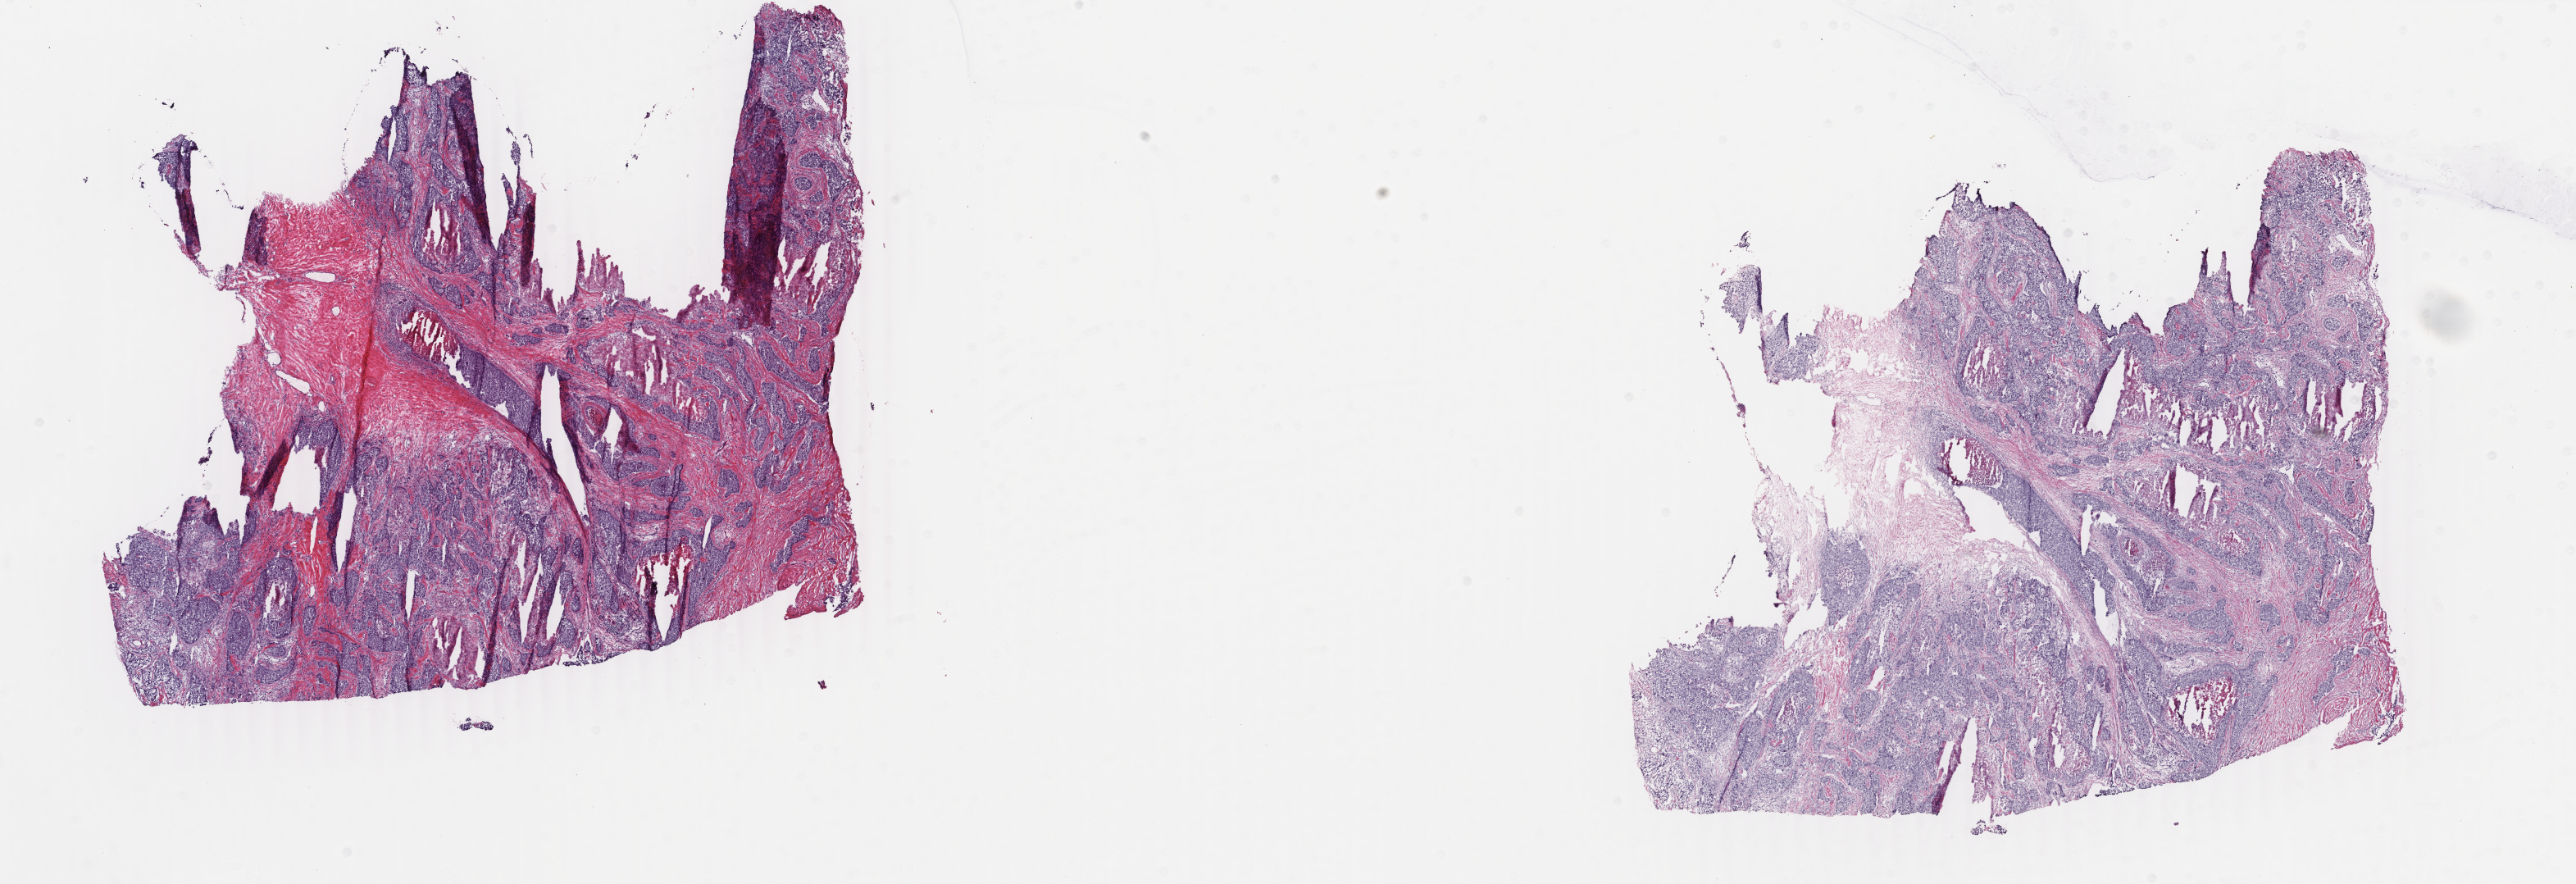
Digitized H&E tissue section (whole slide) — whole scanned area (about 25.0 x 8.6 mm, acquisition: 40x scan) shown as a low-resolution overview. Frozen section. Sample: primary tumour, breast. Female patient; age at initial diagnosis 51 years. Slide review estimates, as recorded: tumour cells 50%, tumour nuclei 80%, normal cells 0%, stromal cells 15%, necrosis 35%. Infiltration values recorded for this section: lymphocyte infiltration 3%, monocyte infiltration 0%, neutrophil infiltration 0%.
• pathologic diagnosis: Infiltrating duct carcinoma, NOS
• laterality: right
• lymph nodes positive (case pathology): 9 of 11 examined